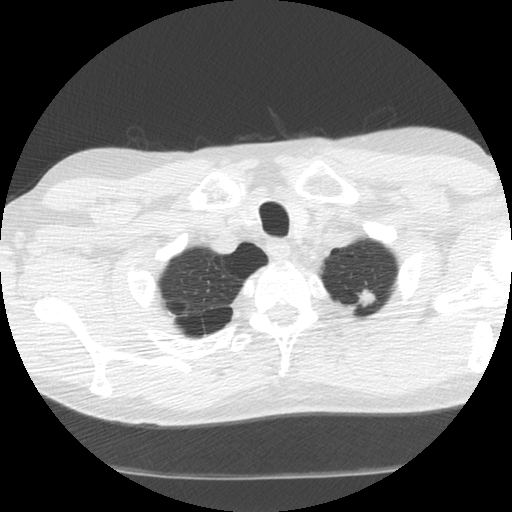
Chest CT (low-dose screening protocol), one axial image, first (baseline) screen, lung window (W 1500 / L -600 HU), 2.5 mm slice thickness, standard (soft-tissue) reconstruction kernel (STANDARD), 140 kVp, slice 118 of 130 in the series. Male, age 63 years at enrolment. Former smoker at enrolment.
Expert-annotated lung lesion, bounding box [x1, y1, x2, y2] px = [340, 279, 388, 324]. The screening reader recorded 4 non-calcified nodules or masses ≥4 mm on this exam (left upper lobe, right upper lobe, right lower lobe, right lower lobe); which of them this box marks is not recorded. Official screen result: positive, change unspecified: nodule(s) >= 4 mm or enlarging nodule(s), mass(es), or other non-specific abnormalities suspicious for lung cancer. Later outcome: lung cancer diagnosed 629 days after this screen — adenocarcinoma, NOS, left upper lobe, moderately differentiated (G2), stage IB (AJCC 6th edition), 14 mm at pathology.